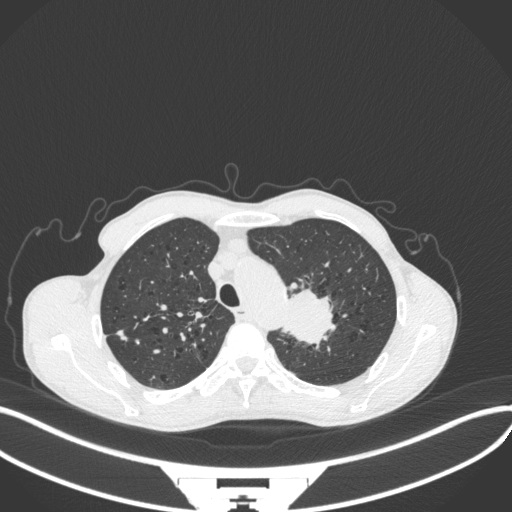
Chest CT, one axial slice; position 327 of 394 along the scan axis; reconstruction kernel B31f; 120 kVp; lung window (W 1500 / L -600 HU); 512 × 512 image matrix. Patient: male, 65 years. From the clinical record (not read from this slice): clinical TNM (as recorded): T2b N0 M0; histopathological grade: G2.
Structures marked on this image (bounding box drawn by a radiologist):
- lung tumour (recorded histology: adenocarcinoma): bounding box (x1, y1, x2, y2) in pixels: (277, 282, 341, 350)